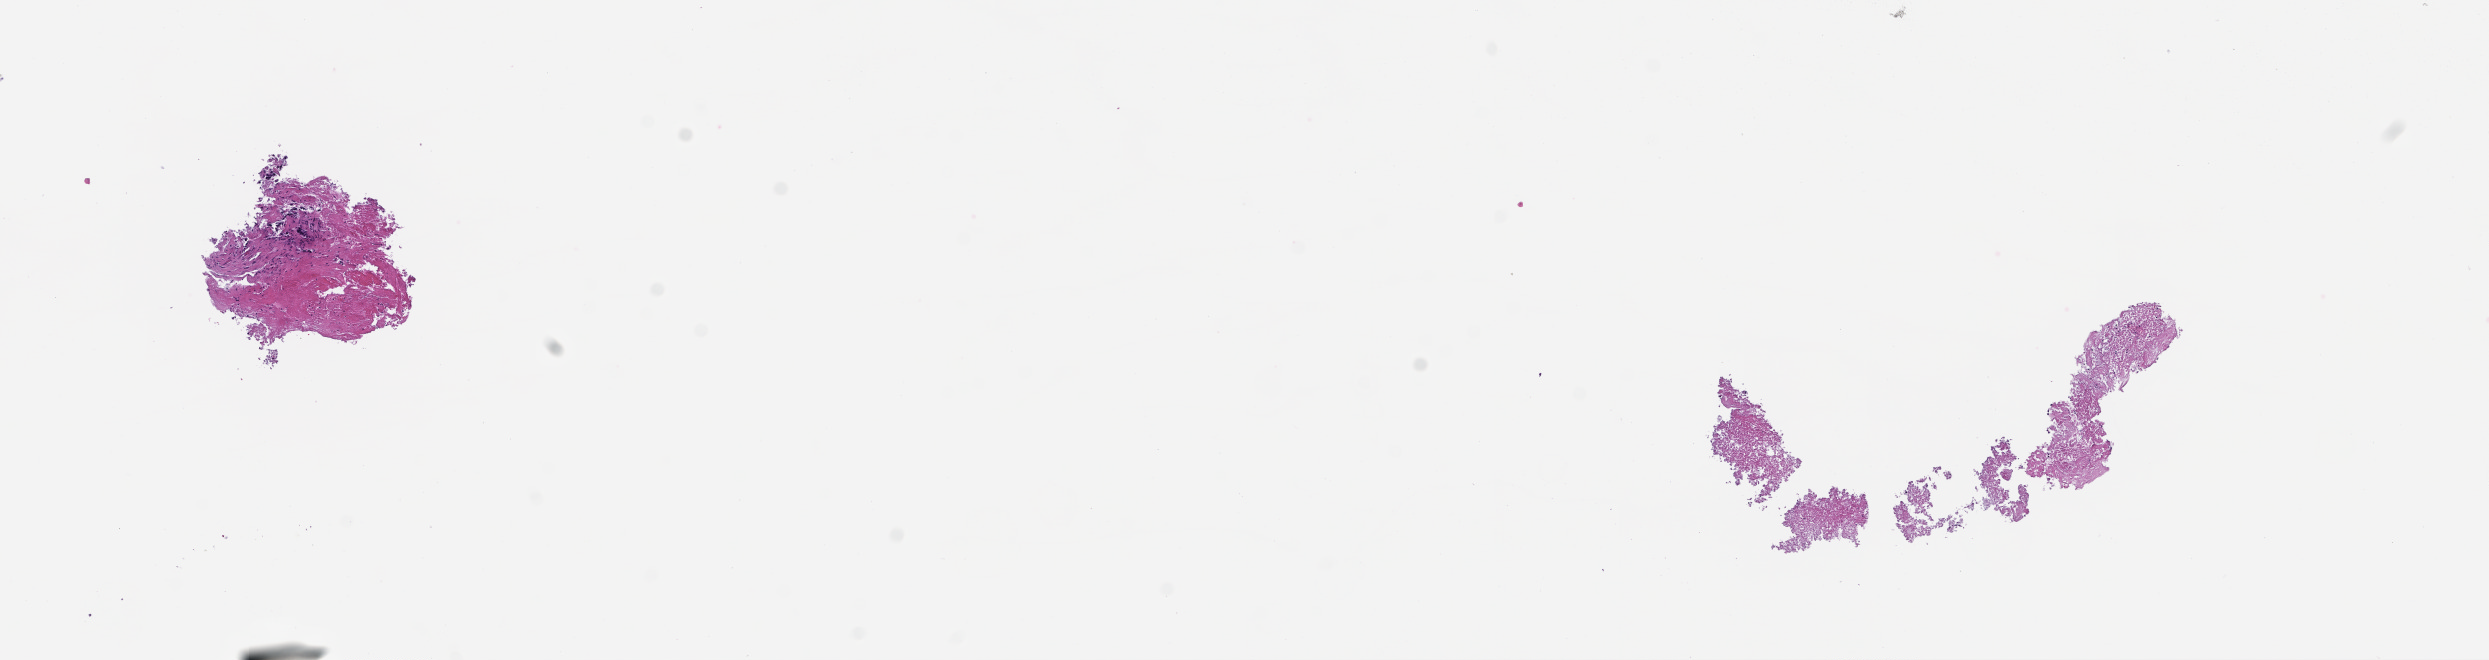
H&E whole-slide image, low-resolution overview of the scanned area, about 10.1 x 2.7 mm, FFPE section, collected at baseline (before treatment). Female patient.
- this section: metastasis (sampled organ not recorded)
- patient diagnosis (primary): Colorectal Carcinoma